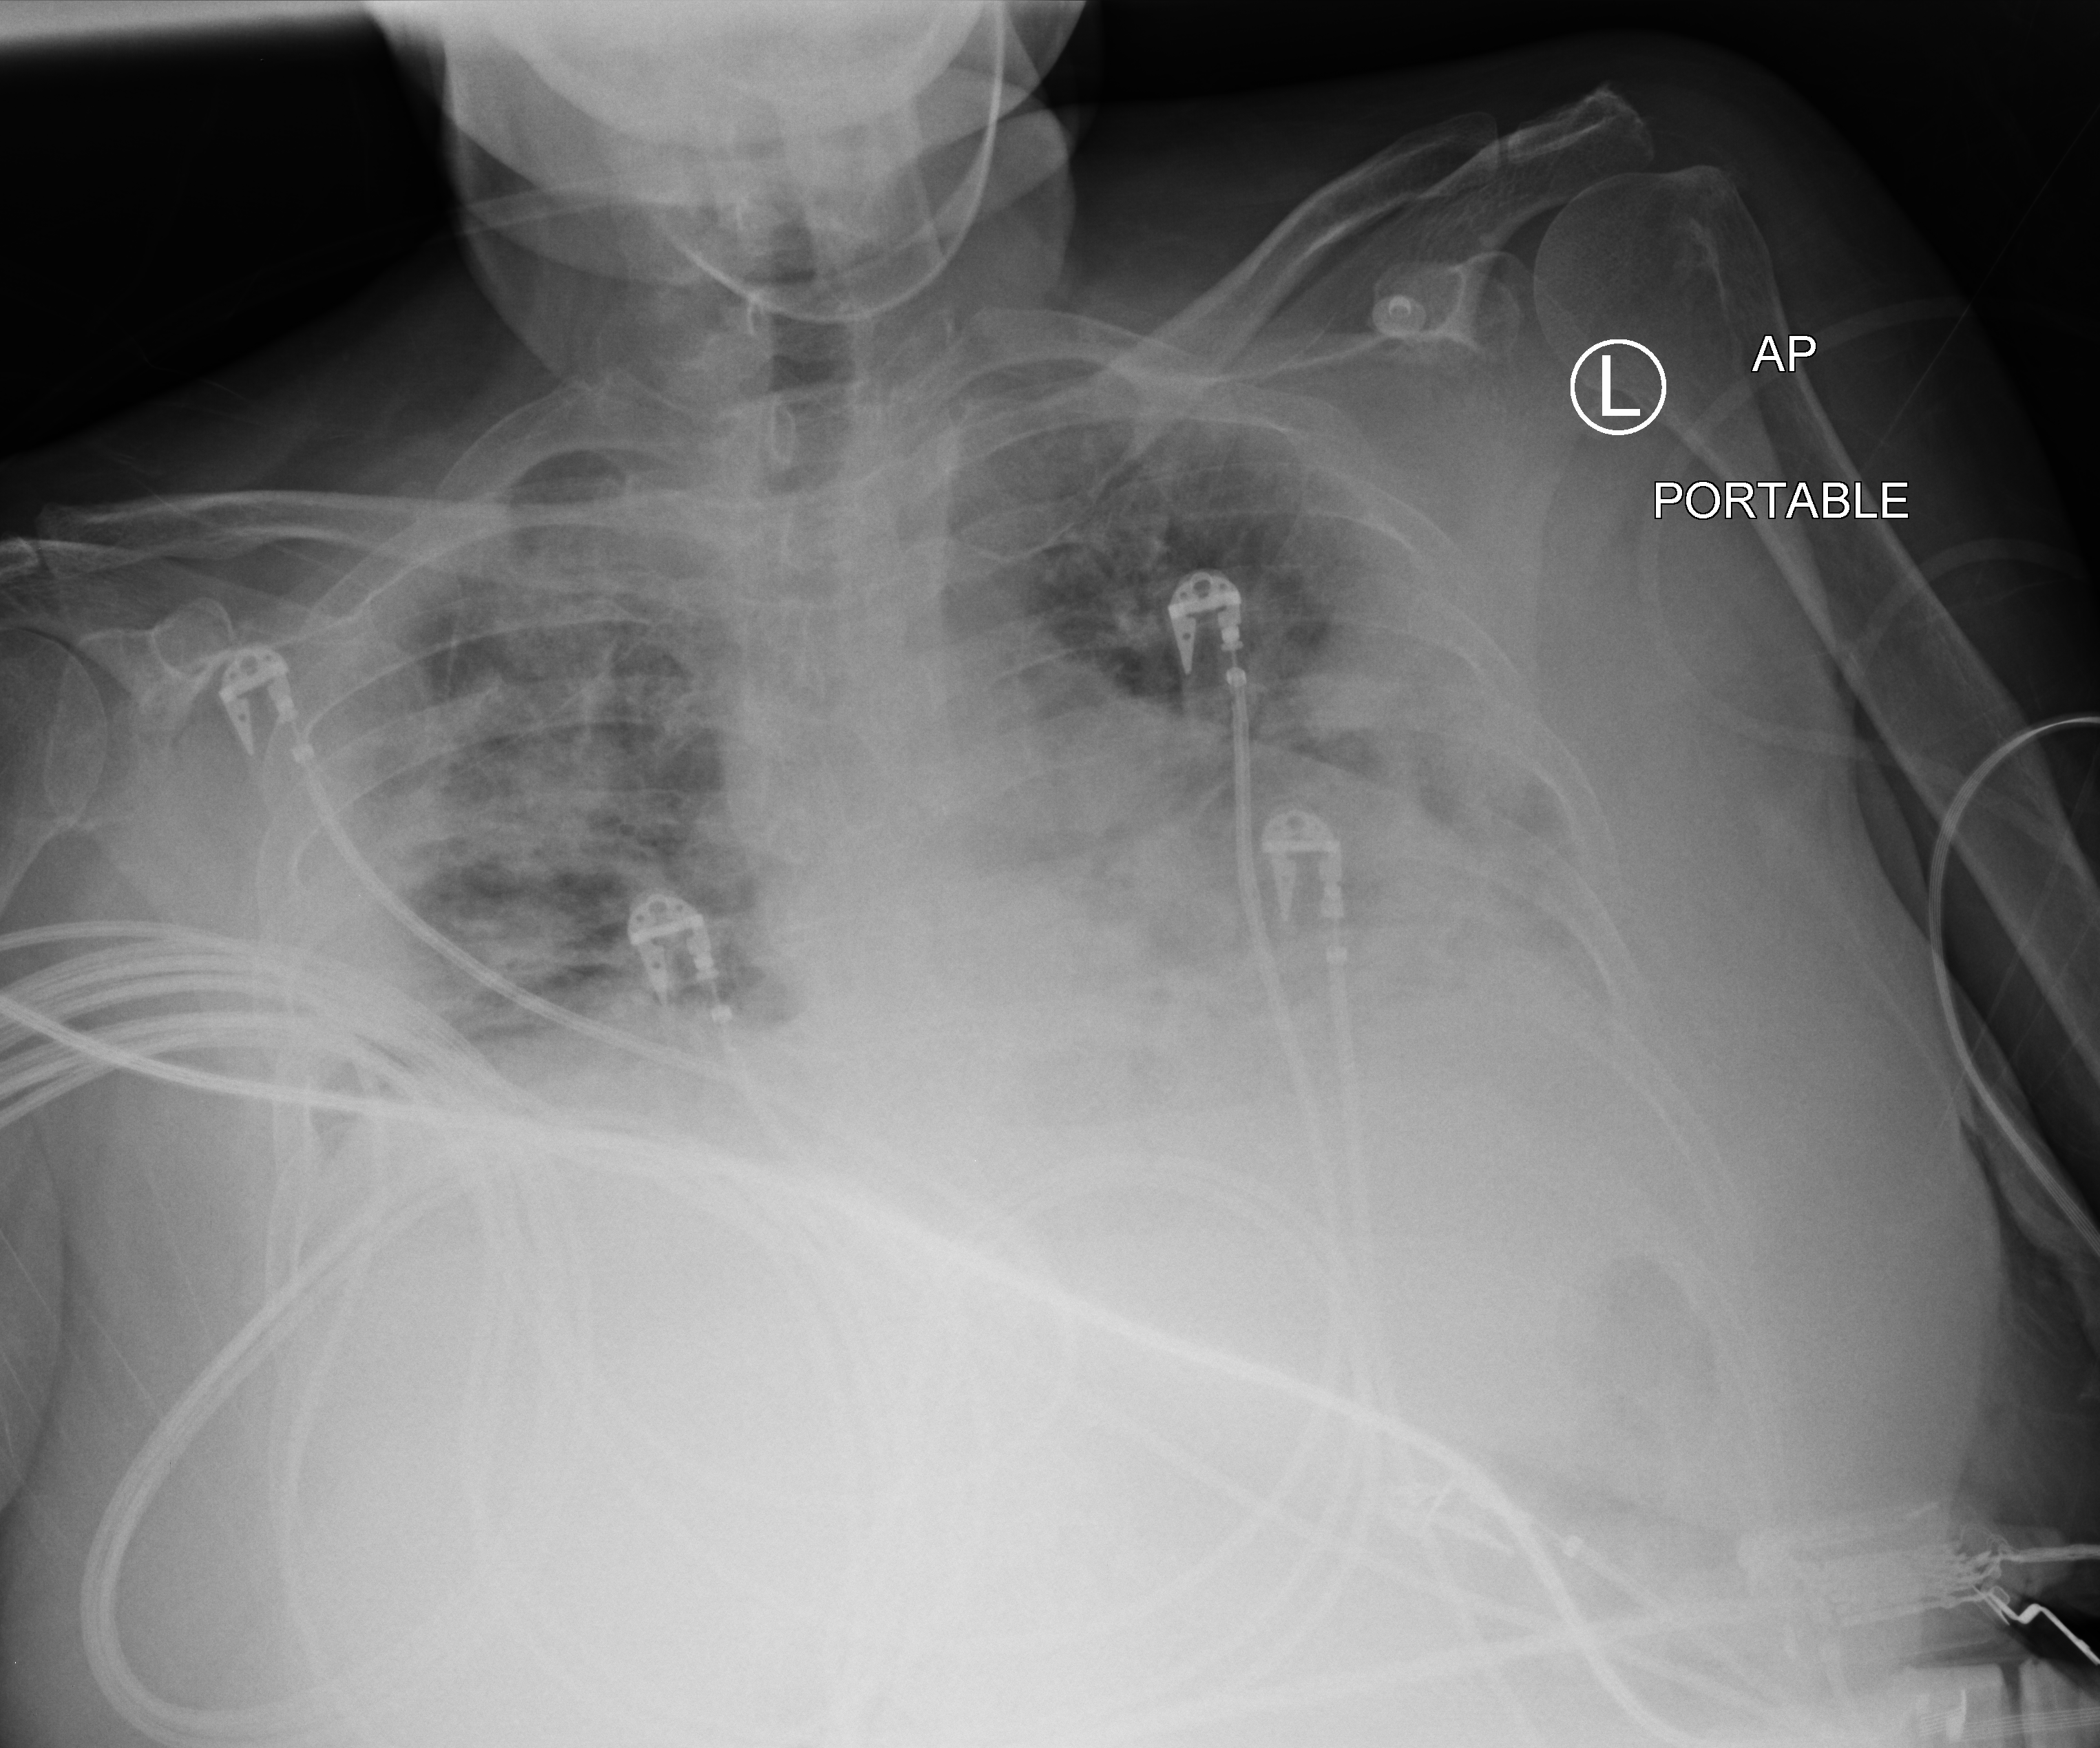
Chest X-ray (portable), anteroposterior (AP) projection. Female patient hospitalised with COVID-19, age 18–59 years.
Admission-level facts for this patient (not findings on this image; timing relative to this image not recorded): admitted to intensive care during this hospital stay: yes.